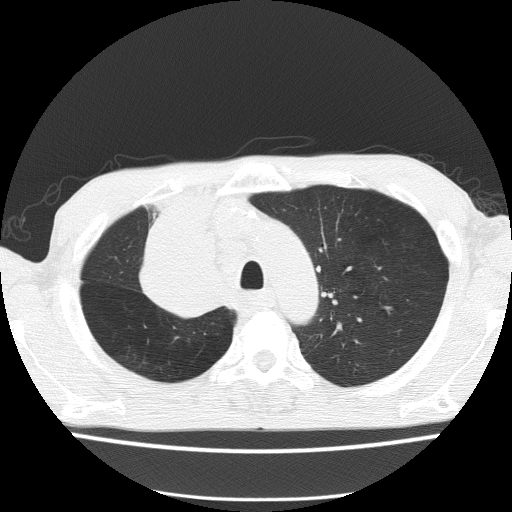
Axial slice from a low-dose chest CT screening exam; baseline annual screen; lung window (W 1500 / L -600 HU); lung (sharp) reconstruction kernel (FC51); 120 kVp; slice 36 of 150 in the series. Male participant, aged 59 years at enrolment. Former smoker at enrolment.
Expert-annotated lung lesion, bounding box [x1, y1, x2, y2] px = [131, 234, 239, 326]. The screening reader recorded 5 non-calcified nodules or masses ≥4 mm on this exam (left upper lobe, left upper lobe, left upper lobe, right middle lobe, right lower lobe); which of them this box marks is not recorded. Lung cancer was diagnosed 72 days after this screen: squamous cell carcinoma, NOS, right upper lobe, moderately differentiated (G2), stage IV (AJCC 6th edition).